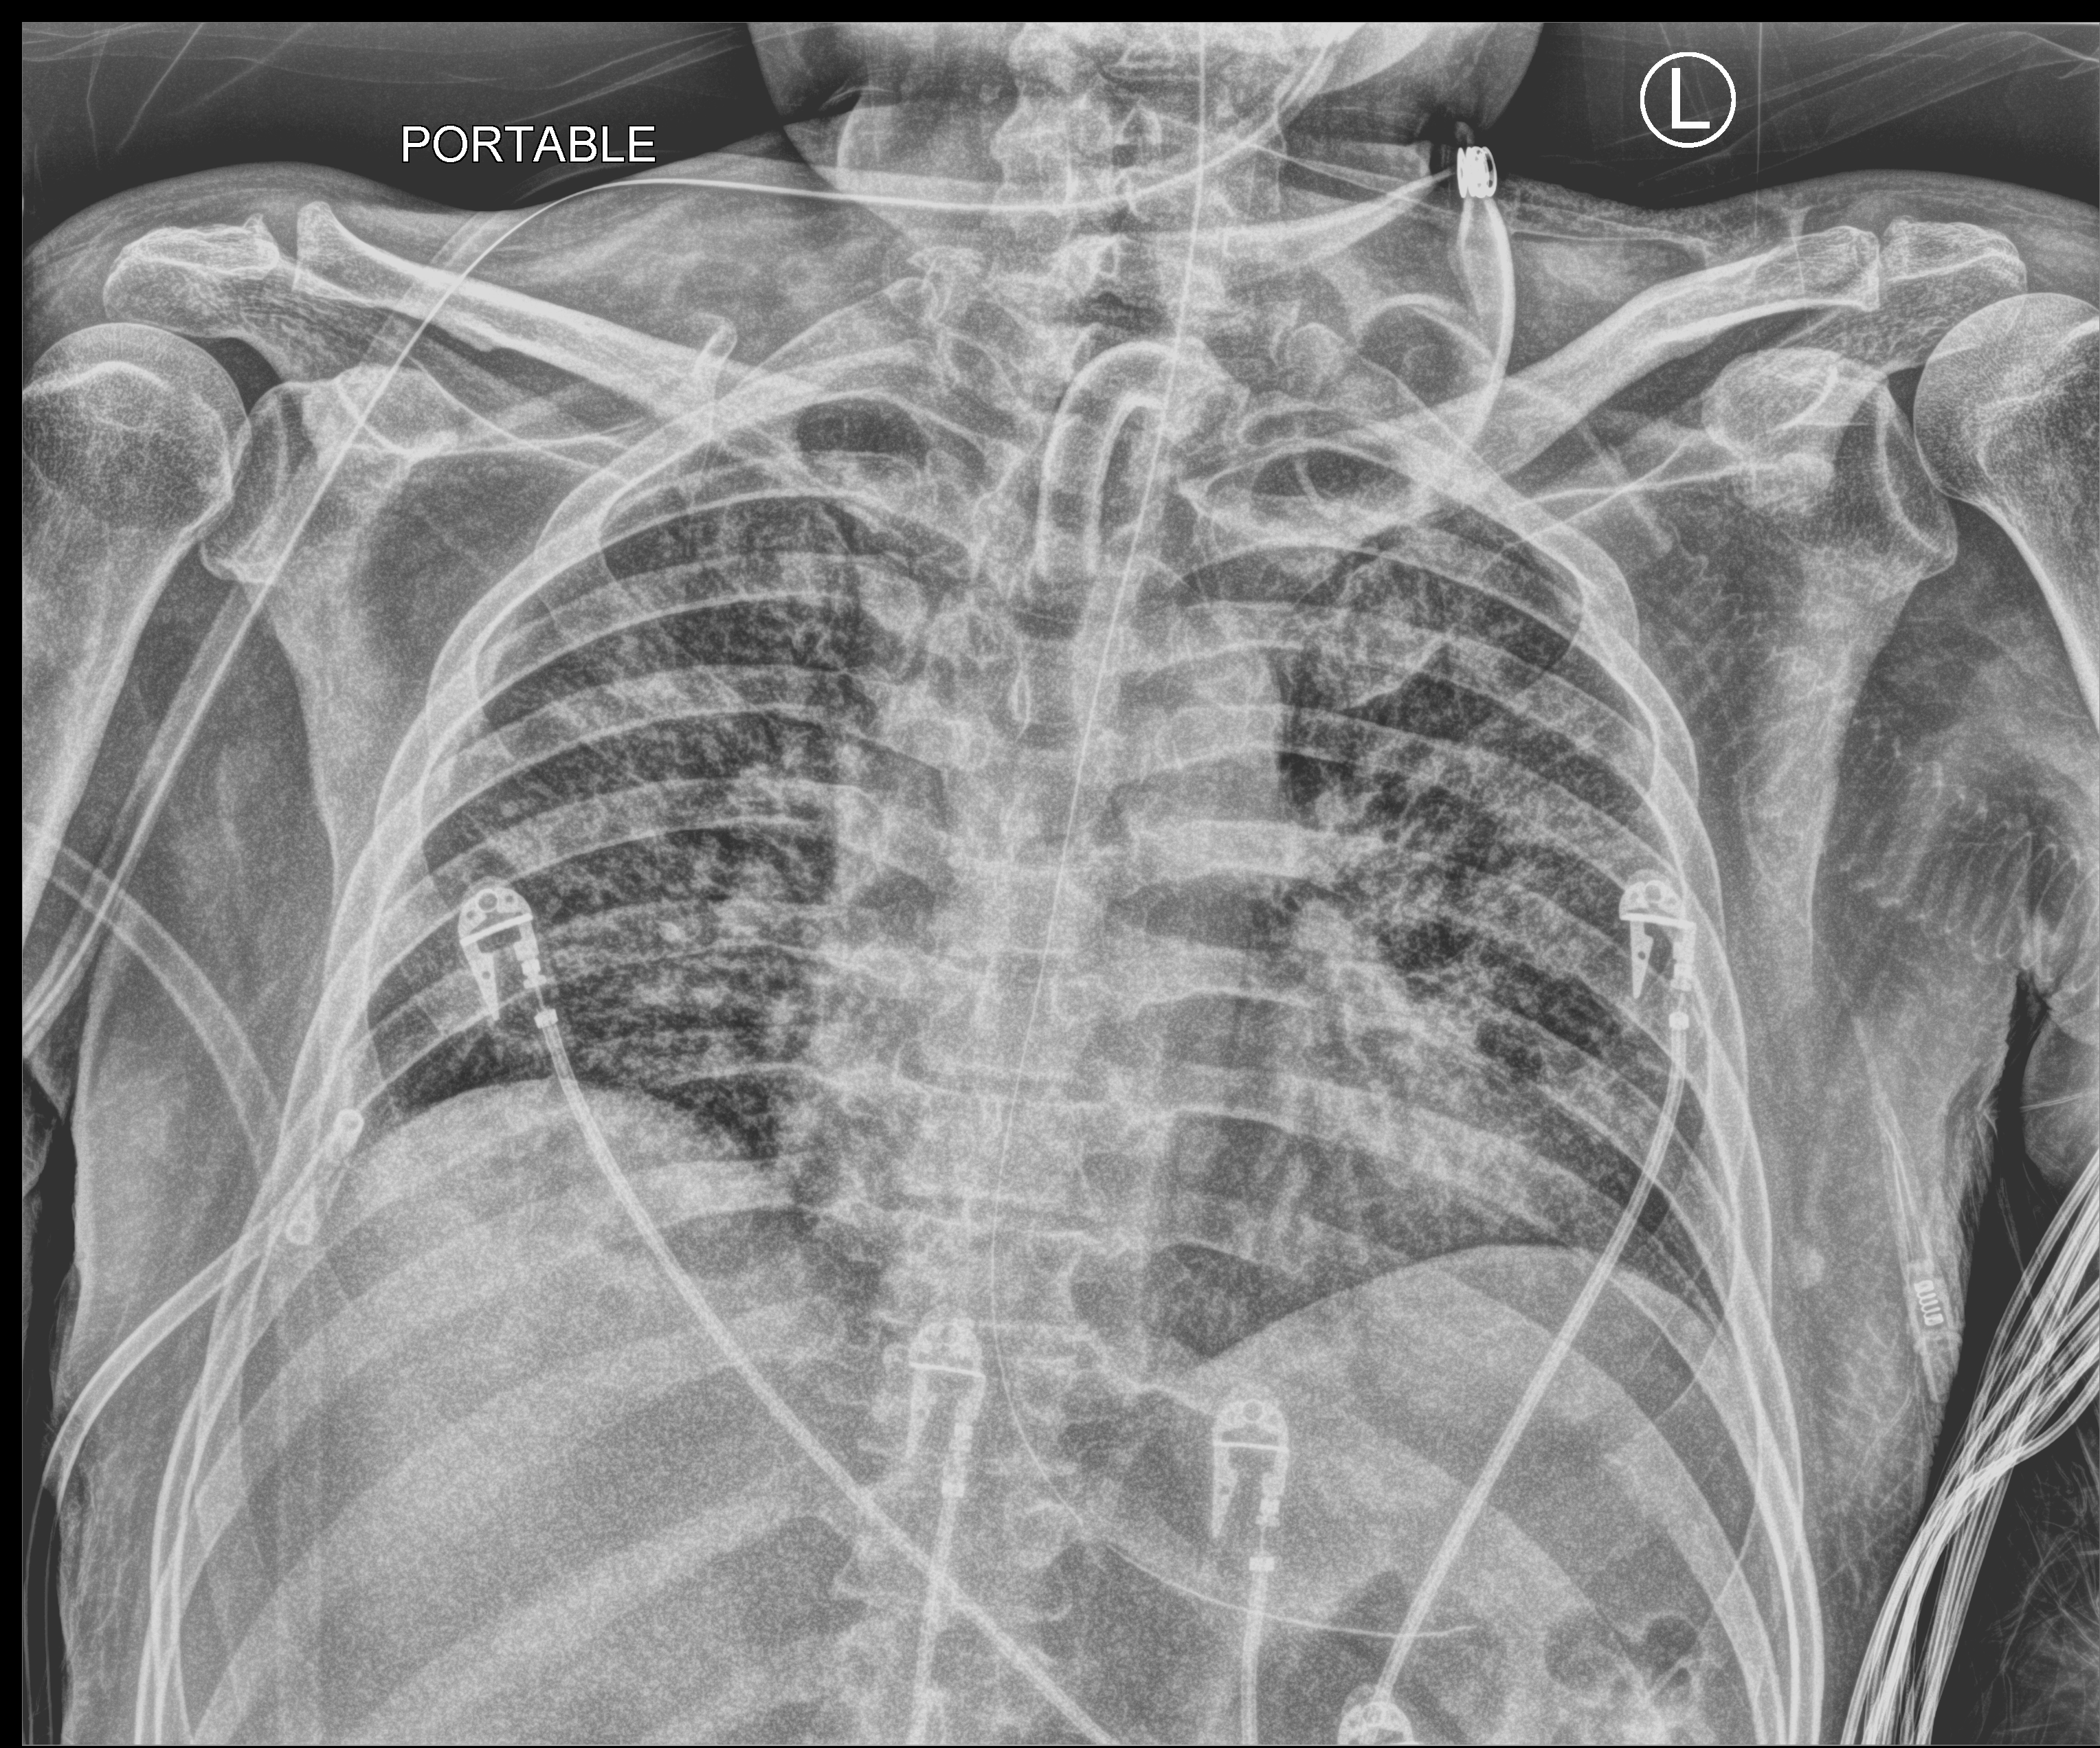
Chest X-ray (portable); anteroposterior (AP) projection. Patient hospitalised with COVID-19; male, aged 18–59 years.
From the hospital-stay record, not from the radiograph (when in the stay this image was taken is not recorded): chronic kidney disease (admission record): no.